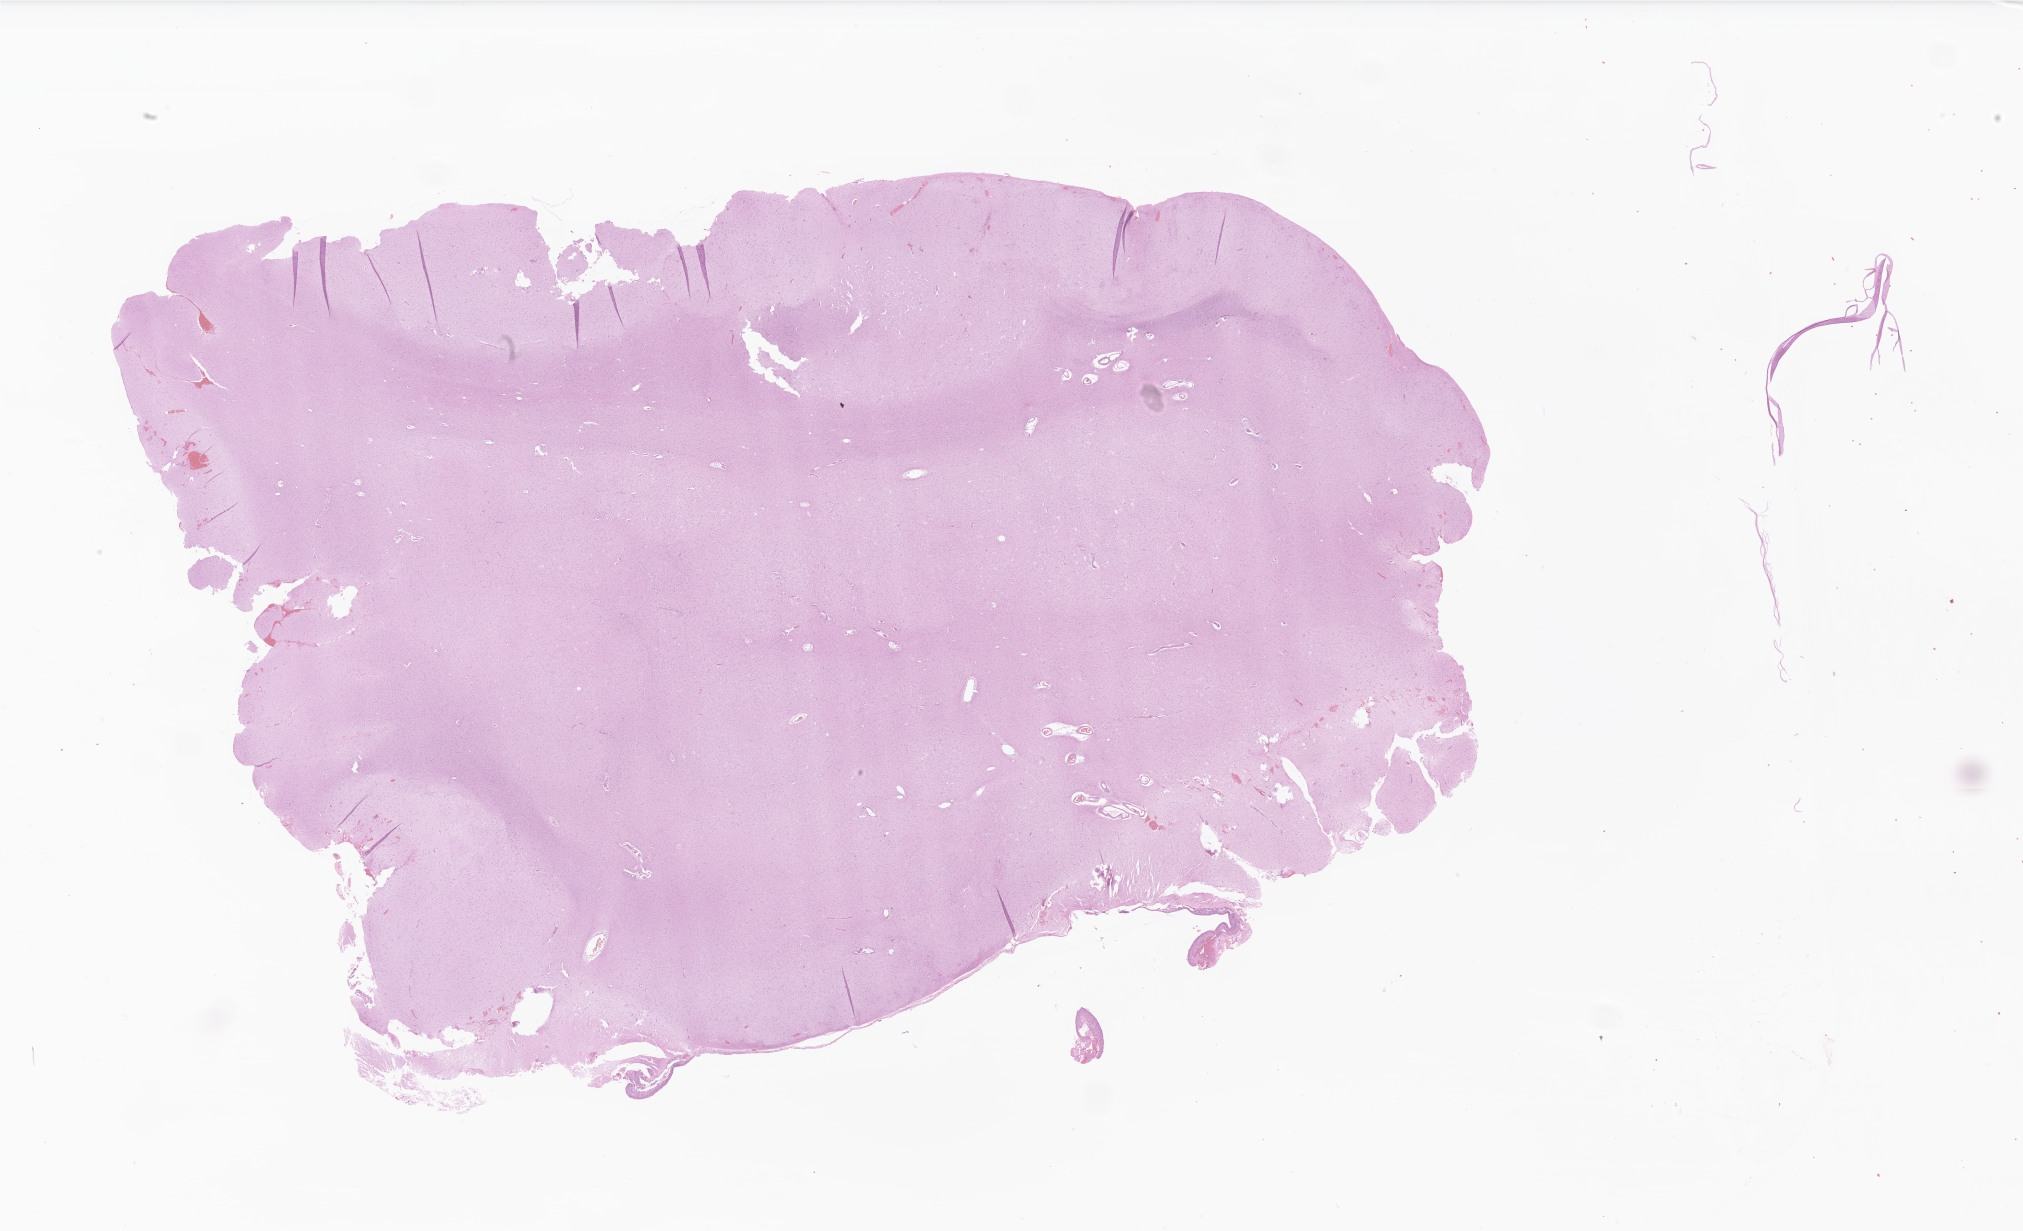
Digitized haematoxylin and eosin-stained section of tumor tissue from the temporal lobe, low-resolution overview of the scanned area, about 34.1 x 20.8 mm. Formalin-fixed, paraffin-embedded (FFPE) tissue. Male patient, age 186 months (15 years 6 months).
- diagnosis (ICD-O-3 morphology term): Dysembryoplastic neuroepithelial tumor